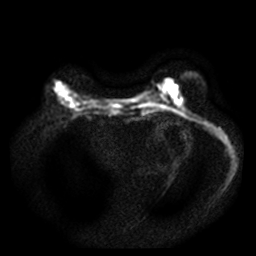
Breast MRI, one axial slice; position 16 of 49 along the scan axis; diffusion-weighted series; image 2 of 4 stored at this slice position (different b-values; order by instance number); 3 T; 256 × 256 image matrix, field of view 340 × 340 mm. Female patient.
Annotated regions visible in this slice (expert manual segmentation):
- tumour on diffusion-weighted imaging: bounding box [x1, y1, x2, y2] px = [60, 91, 67, 97]